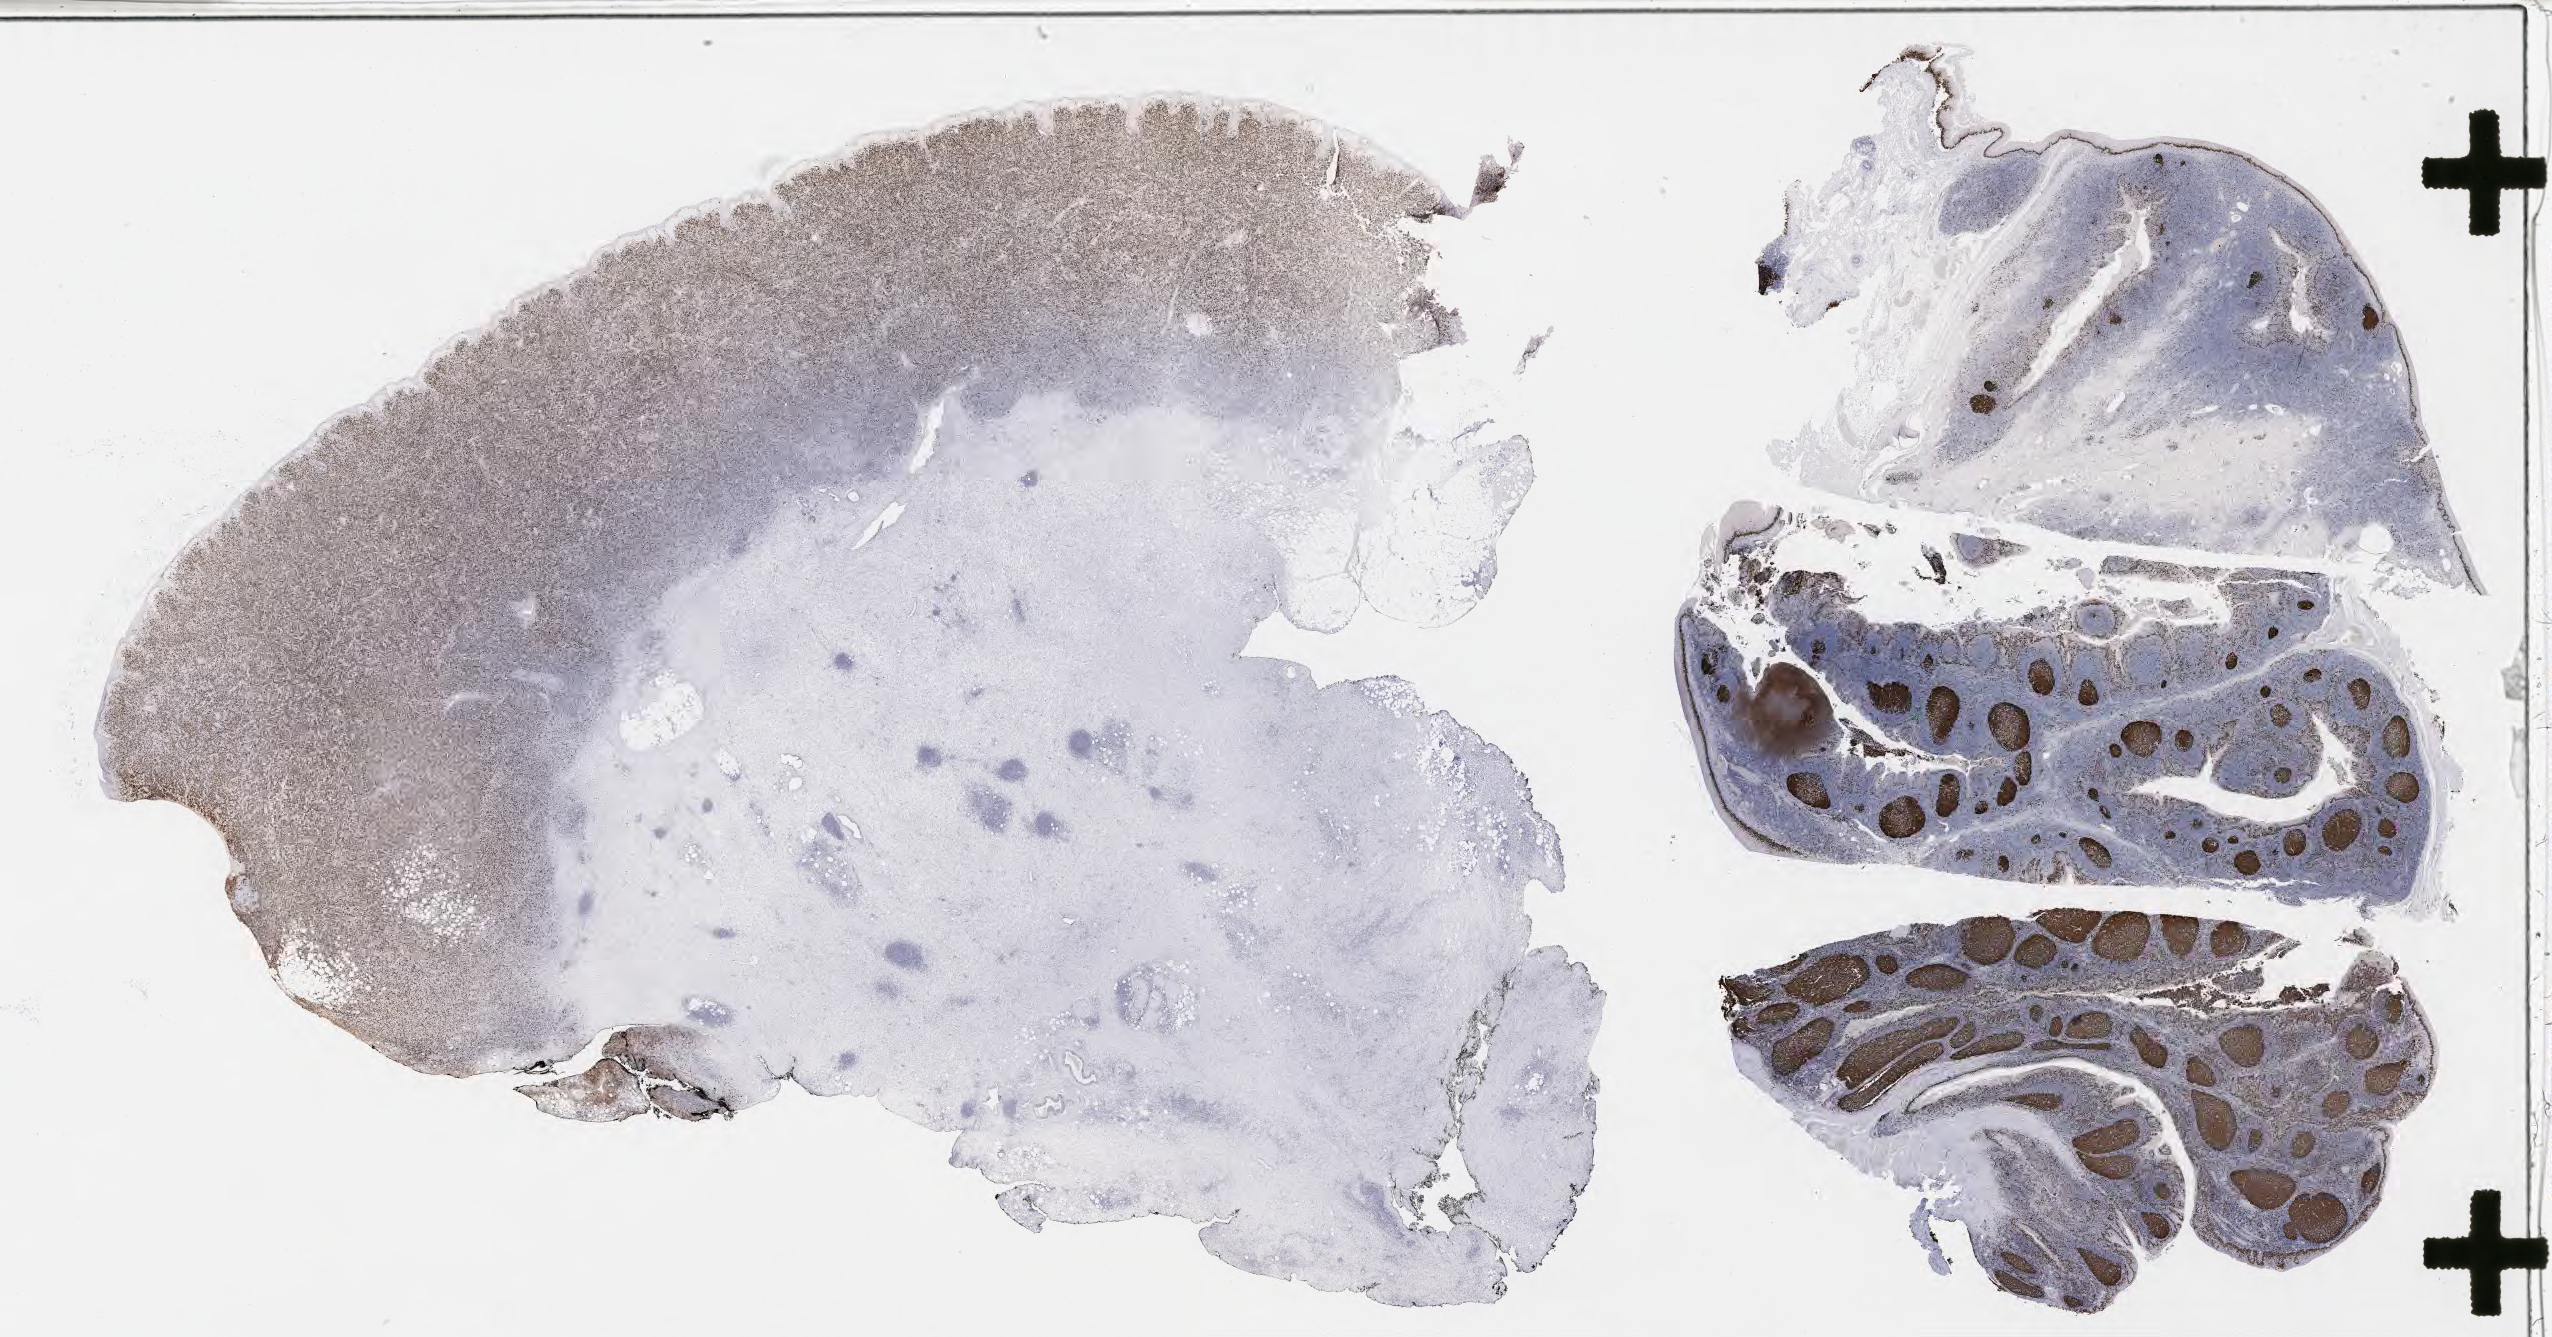
IHC for Ki-67, whole-slide image — low-resolution overview of the scanned area, about 41.2 x 21.6 mm. Tumor tissue. Site: lymph node. Patient: male, 52 years old.
Diagnosis: Diffuse large B-cell lymphoma, NOS.